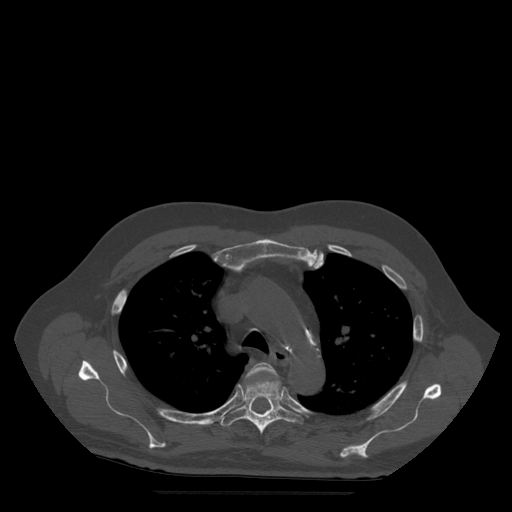
CT including the spine, one axial slice; position 377 of 522 along the scan axis; bone window (W 1800 / L 400 HU); 1.25 mm slice thickness; 512 × 512 image matrix, field of view 420 × 420 mm. Patient age 72 years. Case-level facts recorded for this patient, not image findings: primary cancer: prostate.
Annotated regions visible in this slice (semi-automatically segmented with operator editing):
- T4 vertebra: bounding box [x1, y1, x2, y2] px = [246, 363, 278, 378]
- T5 vertebra: [220, 372, 302, 434]